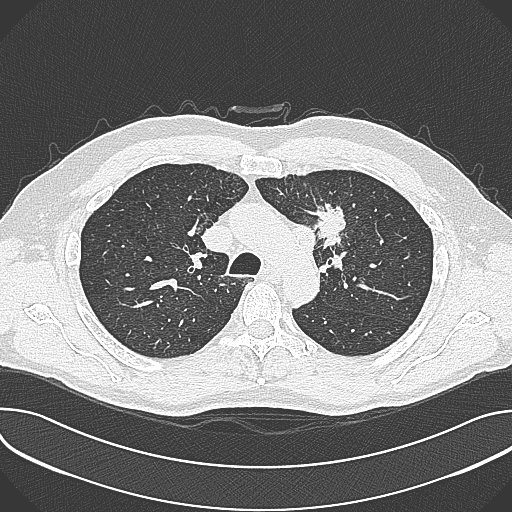
Axial slice from a low-dose chest CT screening exam. Baseline annual screen. Lung window (W 1500 / L -600 HU). 1 mm slice thickness. Lung (sharp) reconstruction kernel (B80f). Slice 98 of 361 in the series. Male, age 59 years at enrolment.
Expert reader's lesion annotation, bounding box <302,198,360,257> (left, top, right, bottom; pixels). The screening reader recorded 2 non-calcified nodules or masses ≥4 mm on this exam (left upper lobe, left upper lobe); which of them this box marks is not recorded. Official screen result: positive, change unspecified: nodule(s) >= 4 mm or enlarging nodule(s), mass(es), or other non-specific abnormalities suspicious for lung cancer. Later outcome: lung cancer diagnosed 21 days after this screen — non-small cell carcinoma, left upper lobe, poorly differentiated (G3), stage IIIA (AJCC 6th edition), 35 mm at pathology.